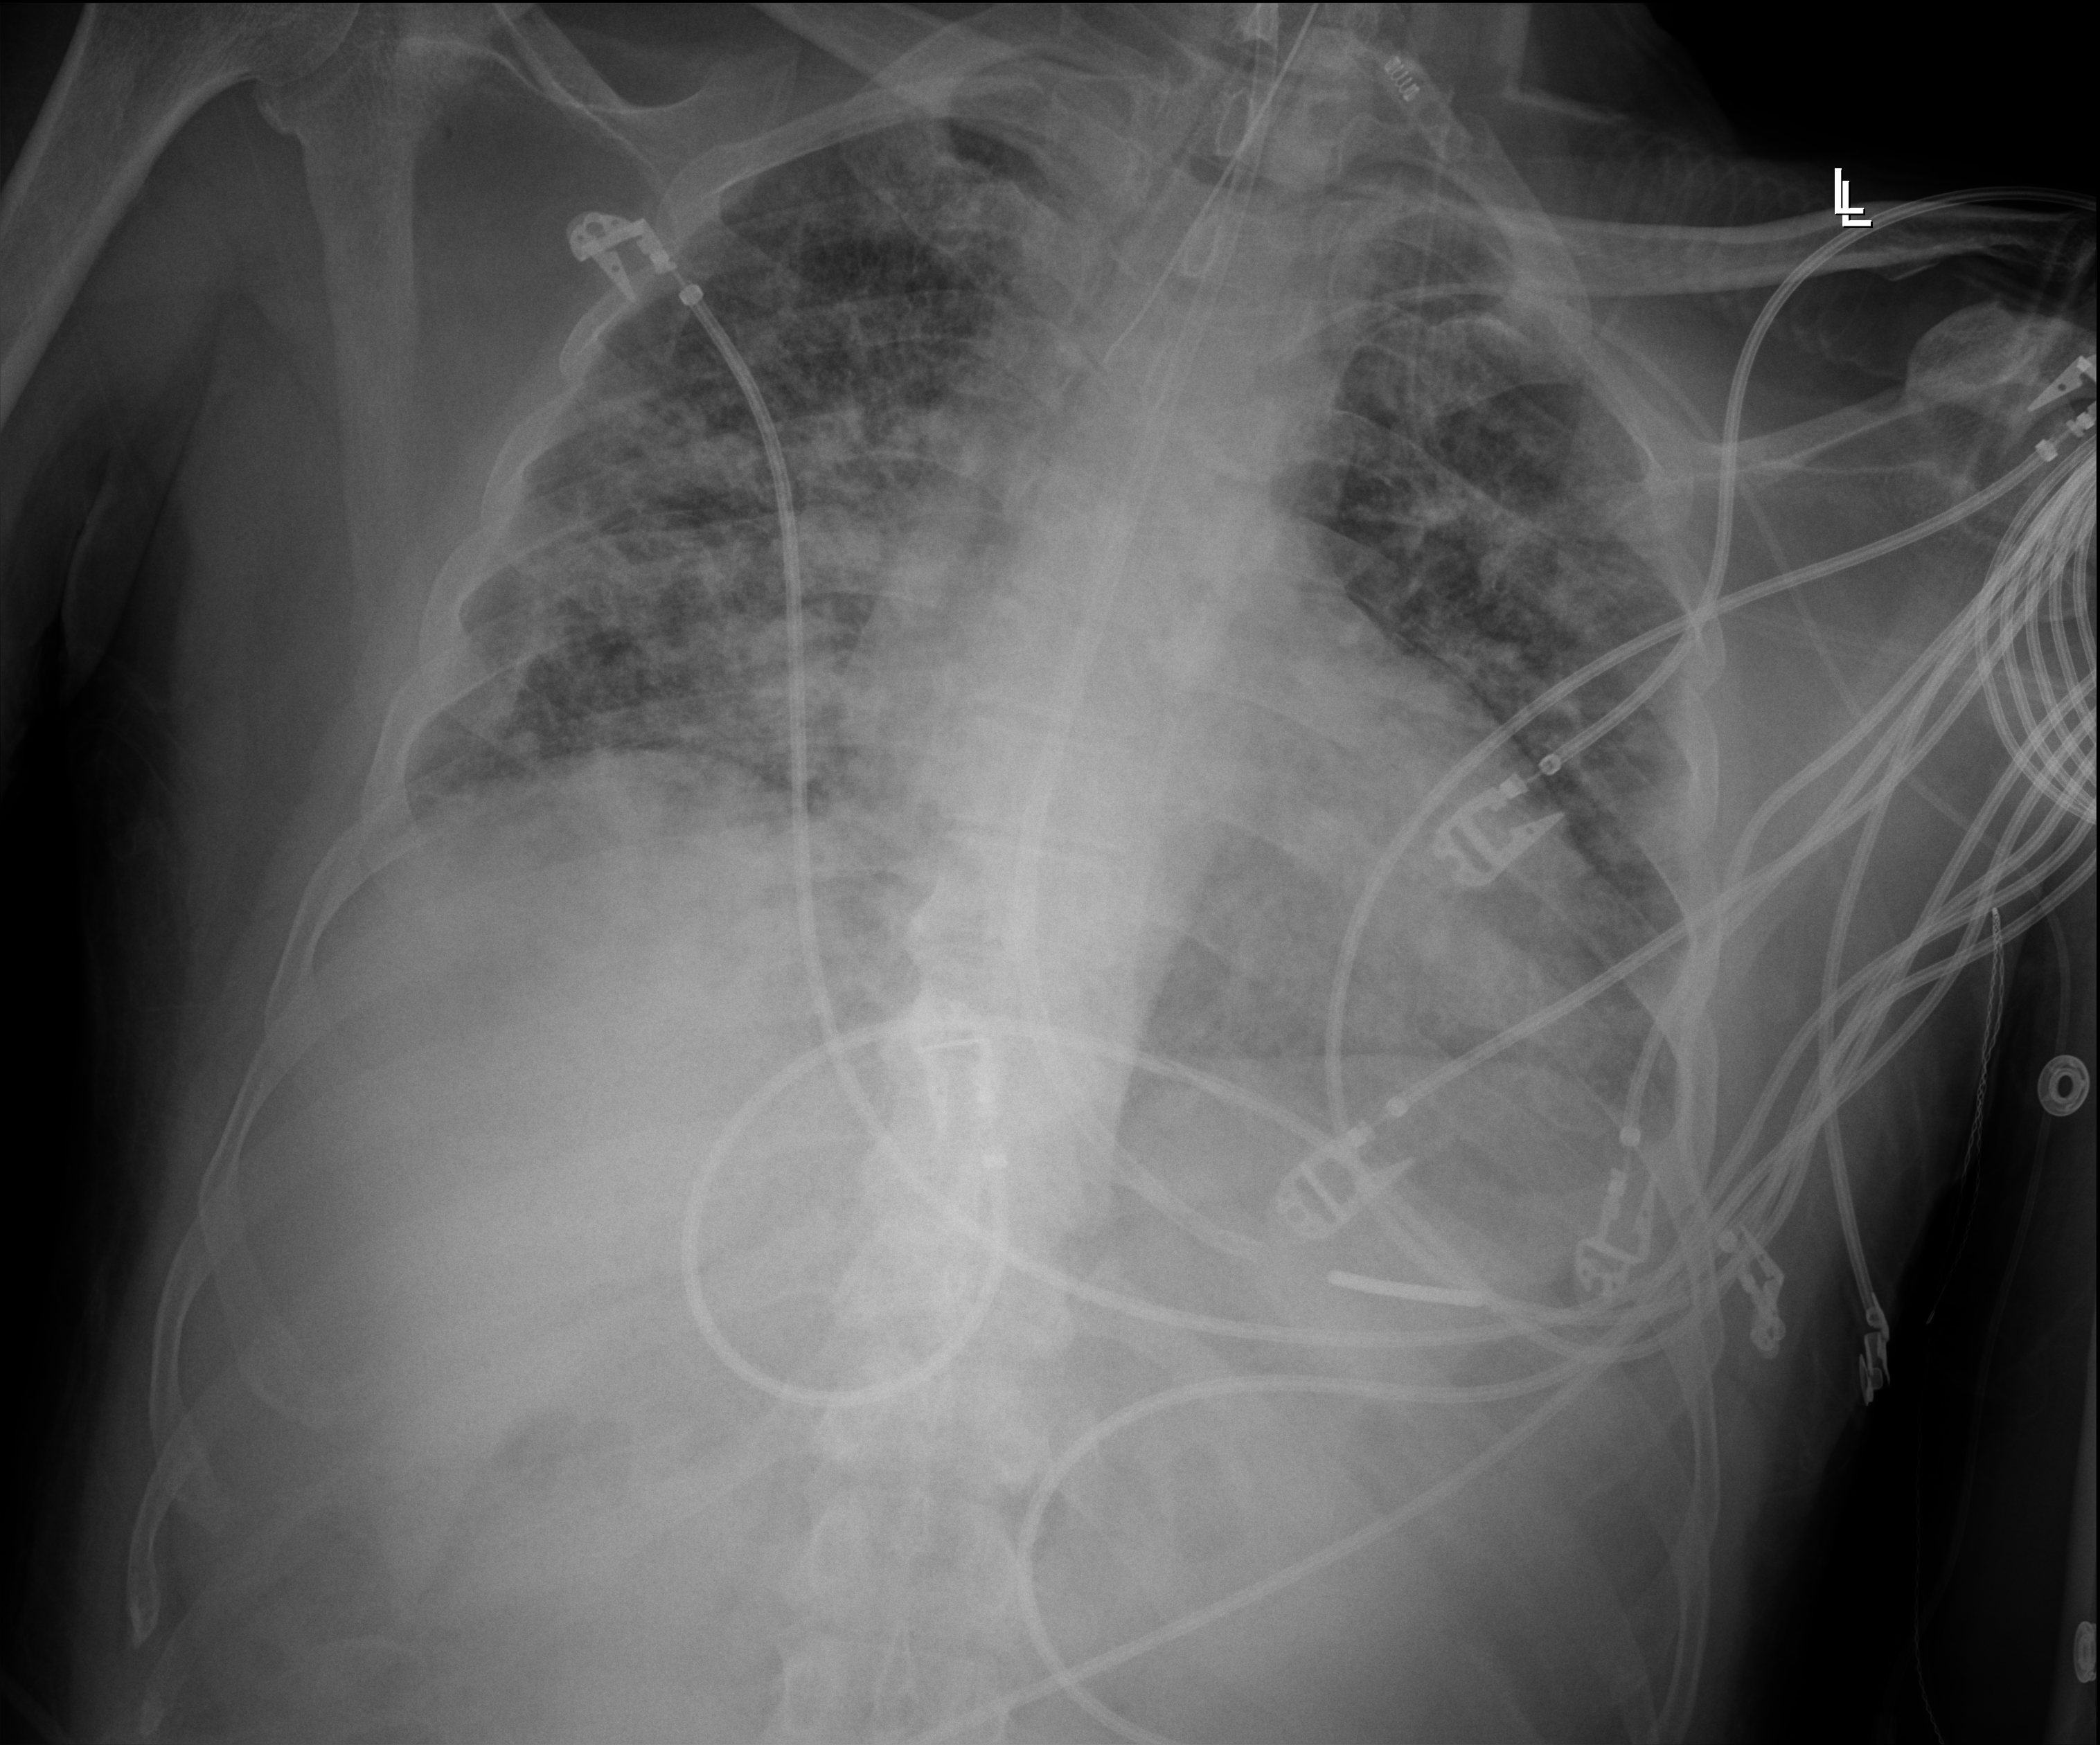
Bedside chest radiograph (digital radiography). Male patient hospitalised with COVID-19, age 18–59 years.
Admission-level facts for this patient (not findings on this image; timing relative to this image not recorded): admitted to intensive care during this hospital stay: yes; mechanically ventilated during this hospital stay: yes; chronic kidney disease (admission record): no.